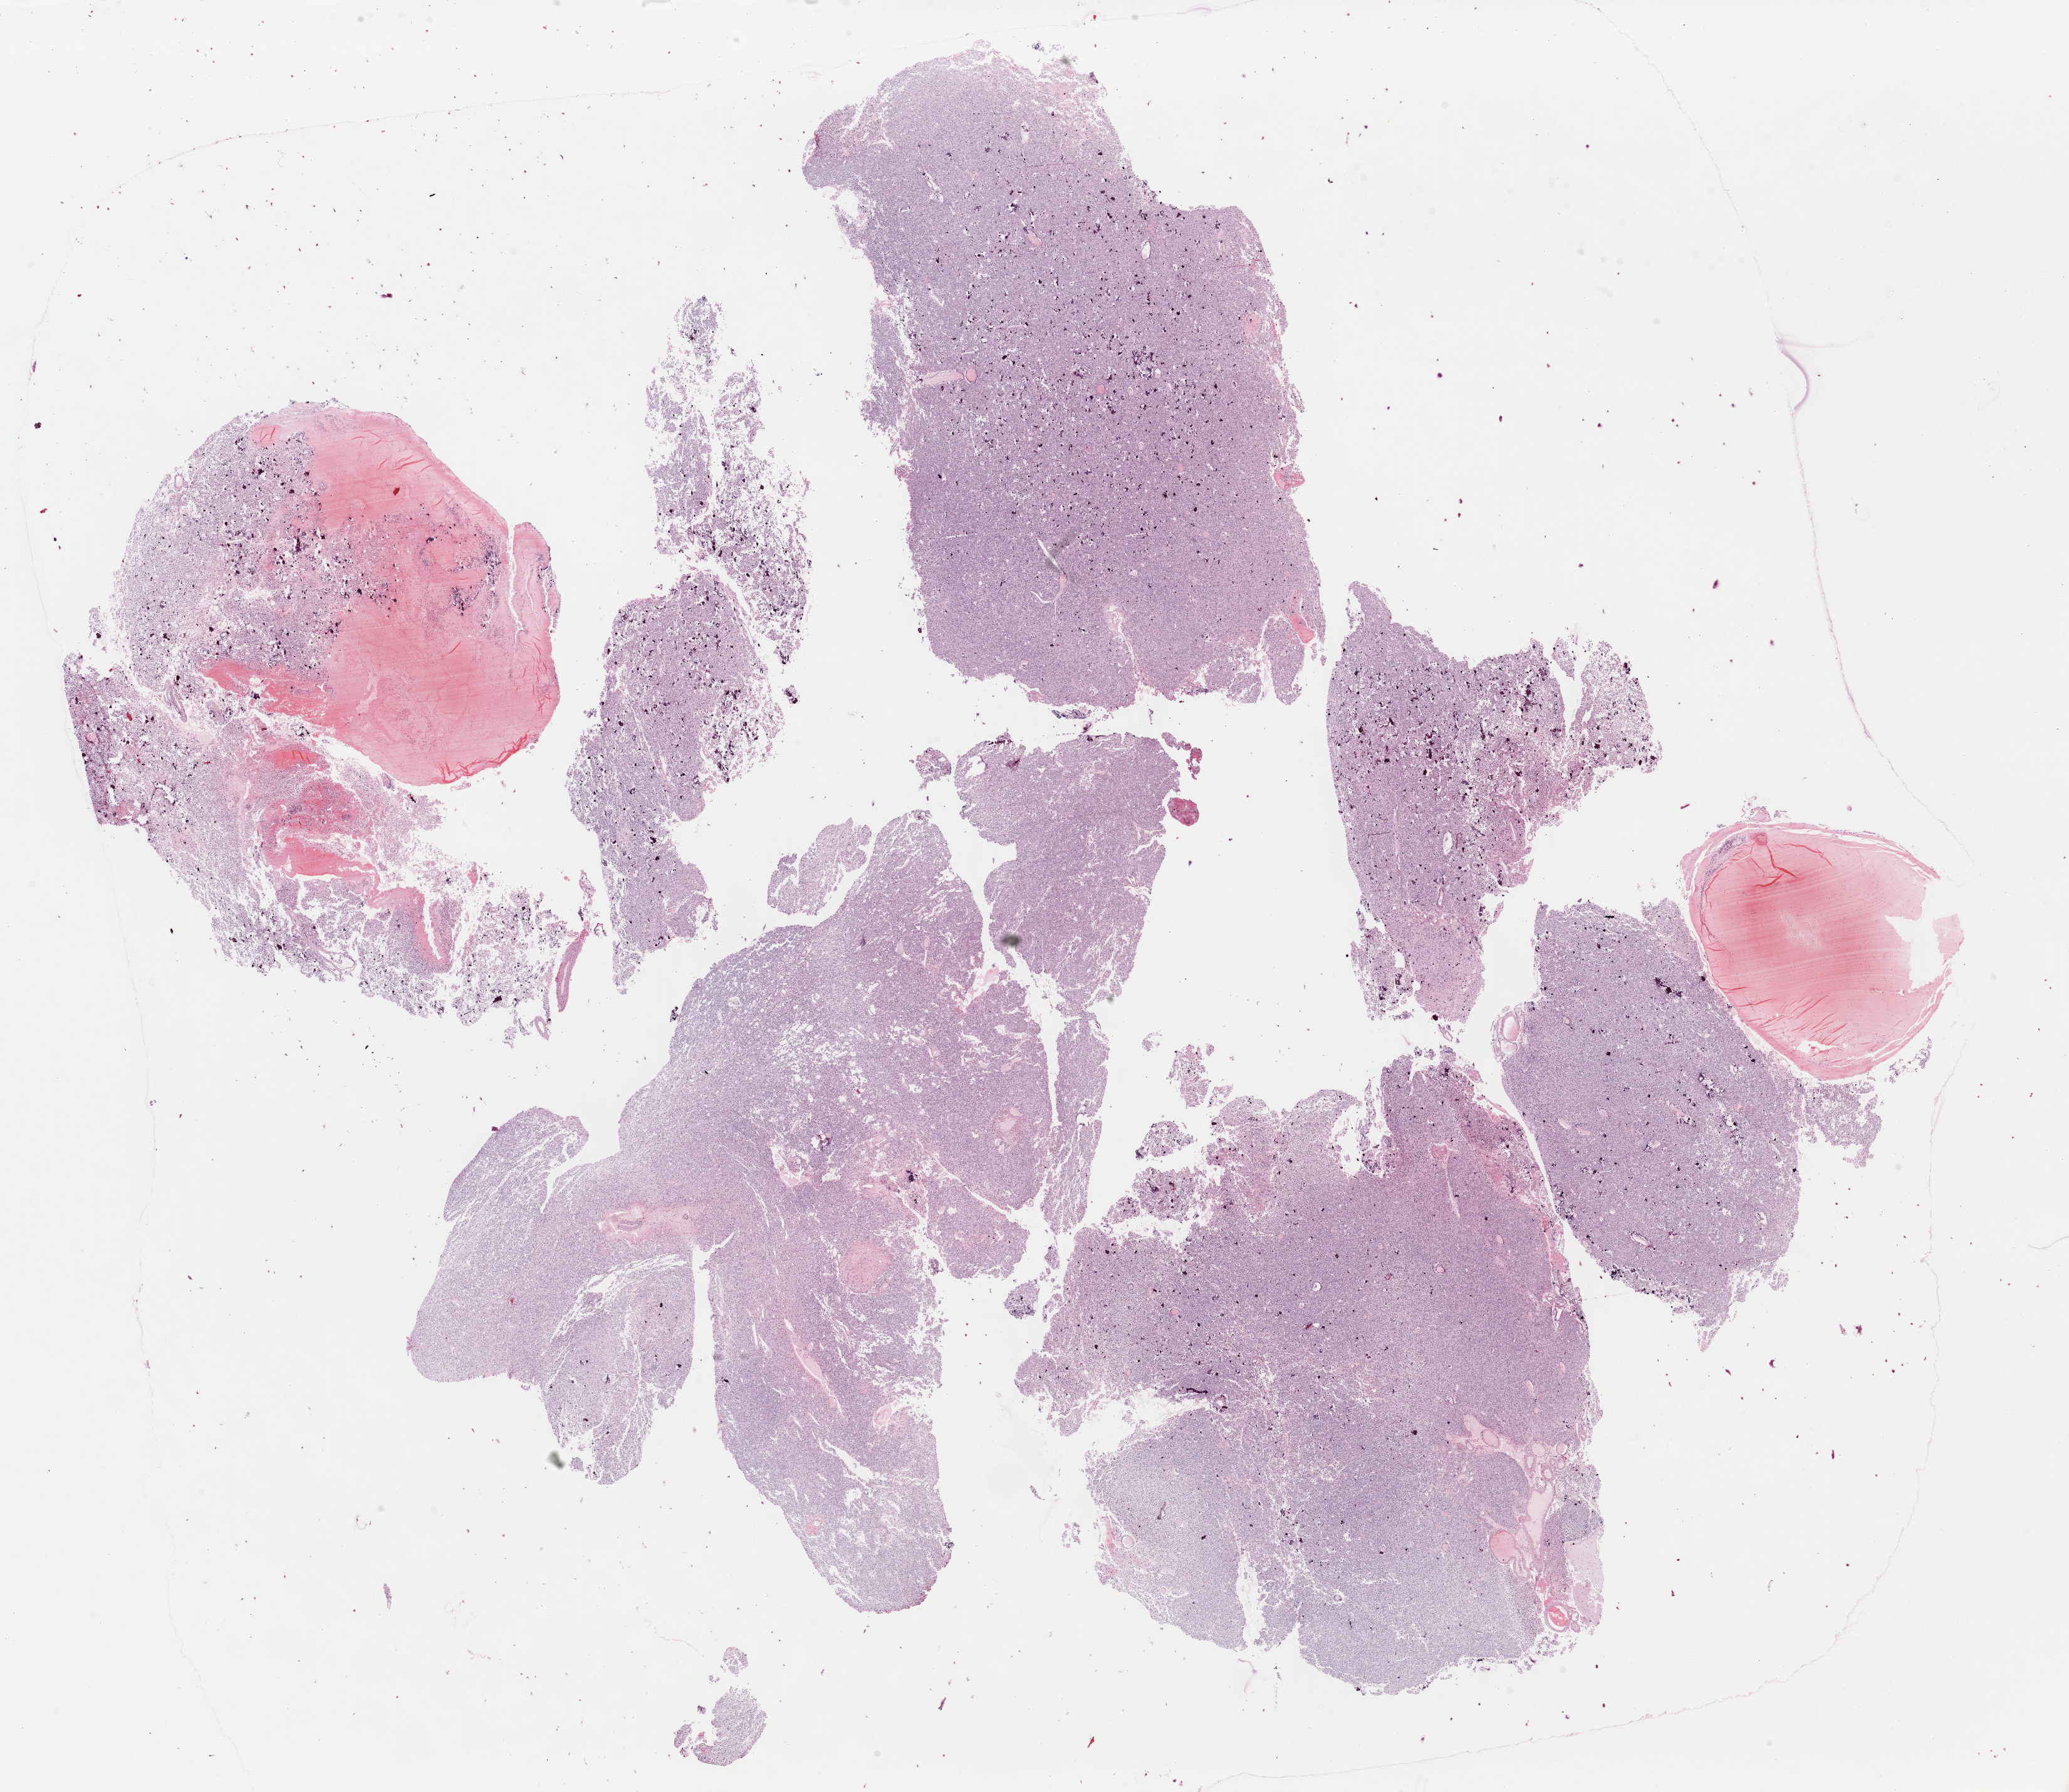
Whole-slide histology image, Hematoxylin and eosin (H&E) stained, low-resolution overview of the scanned area, about 26.0 x 22.6 mm. FFPE section. Sample: primary tumour, brain. Female, age 38 years at initial diagnosis.
Pathologic diagnosis: Oligodendroglioma, anaplastic.